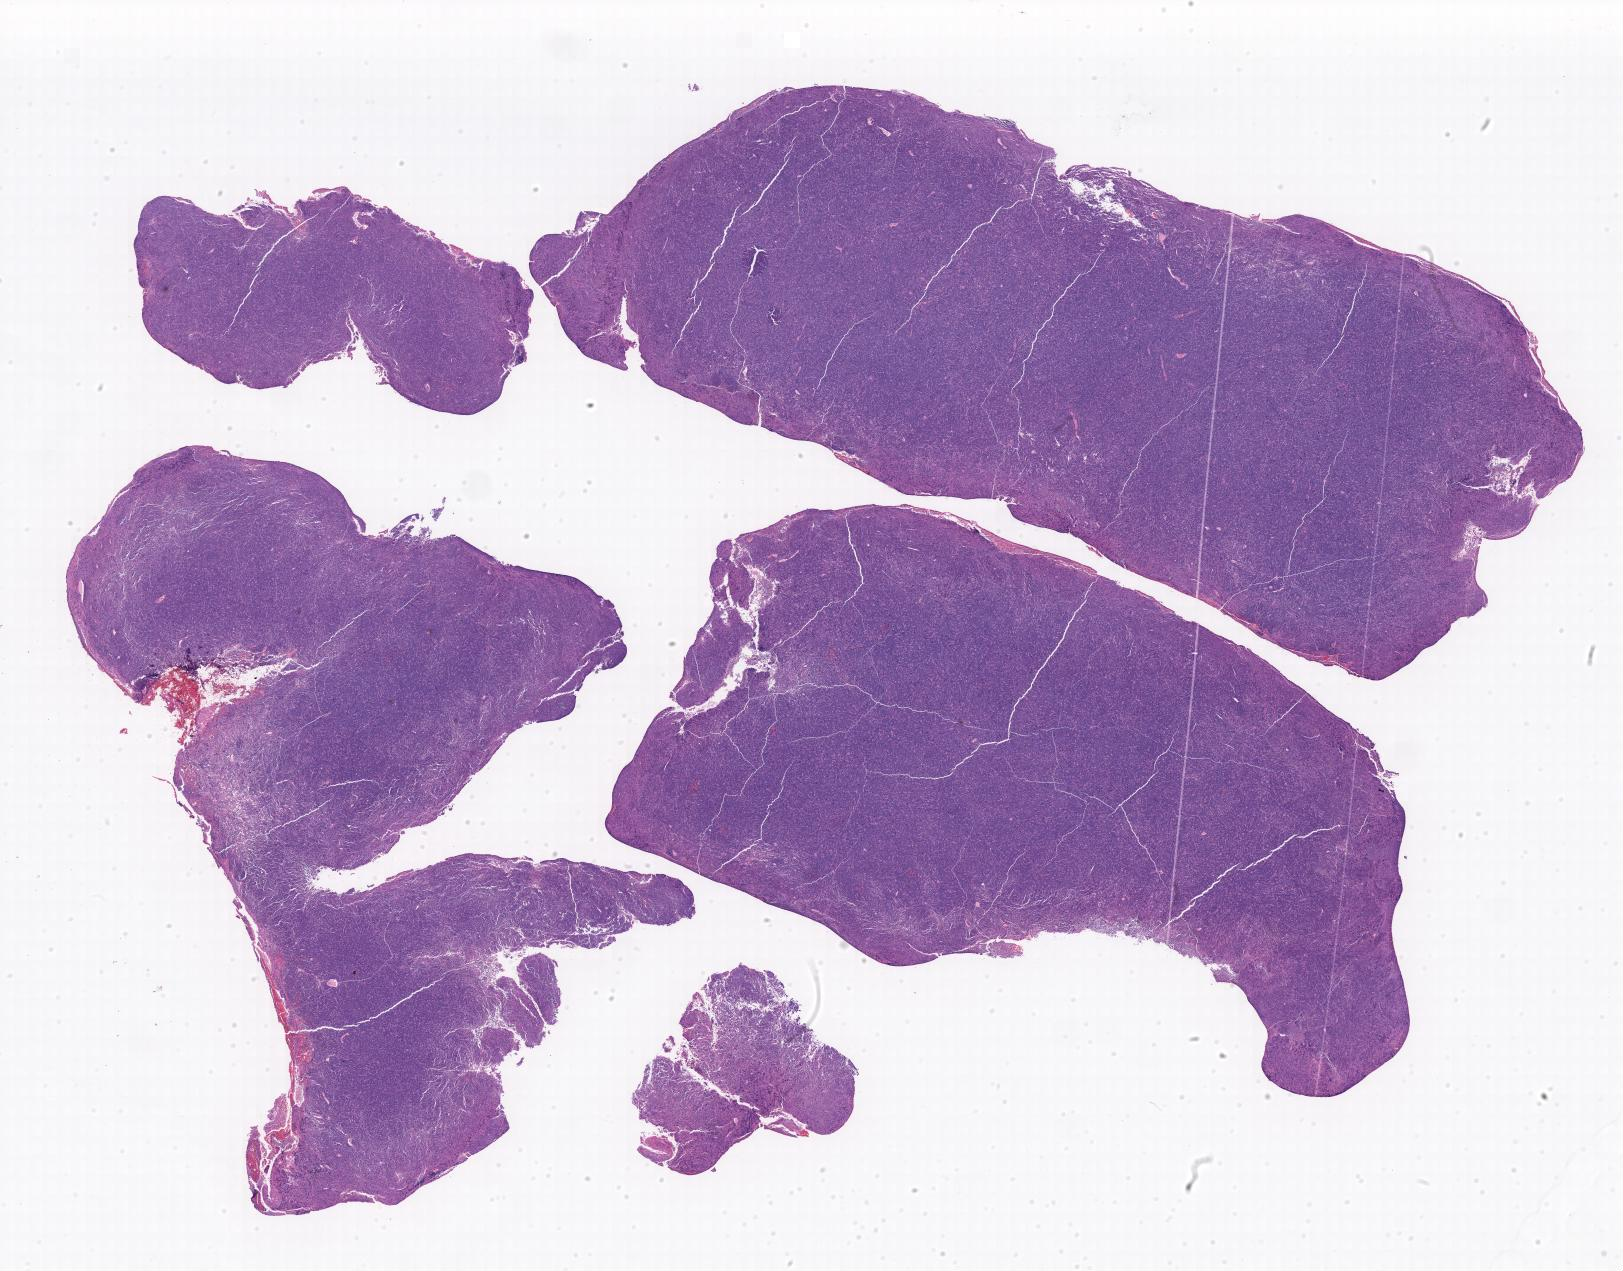
Whole-slide image, H&E stain, a low-resolution overview of the entire scanned area. Tumor tissue. Anatomic site: peritoneum. Female, age 7 years at initial diagnosis.
Histologic diagnosis: Burkitt lymphoma, NOS.